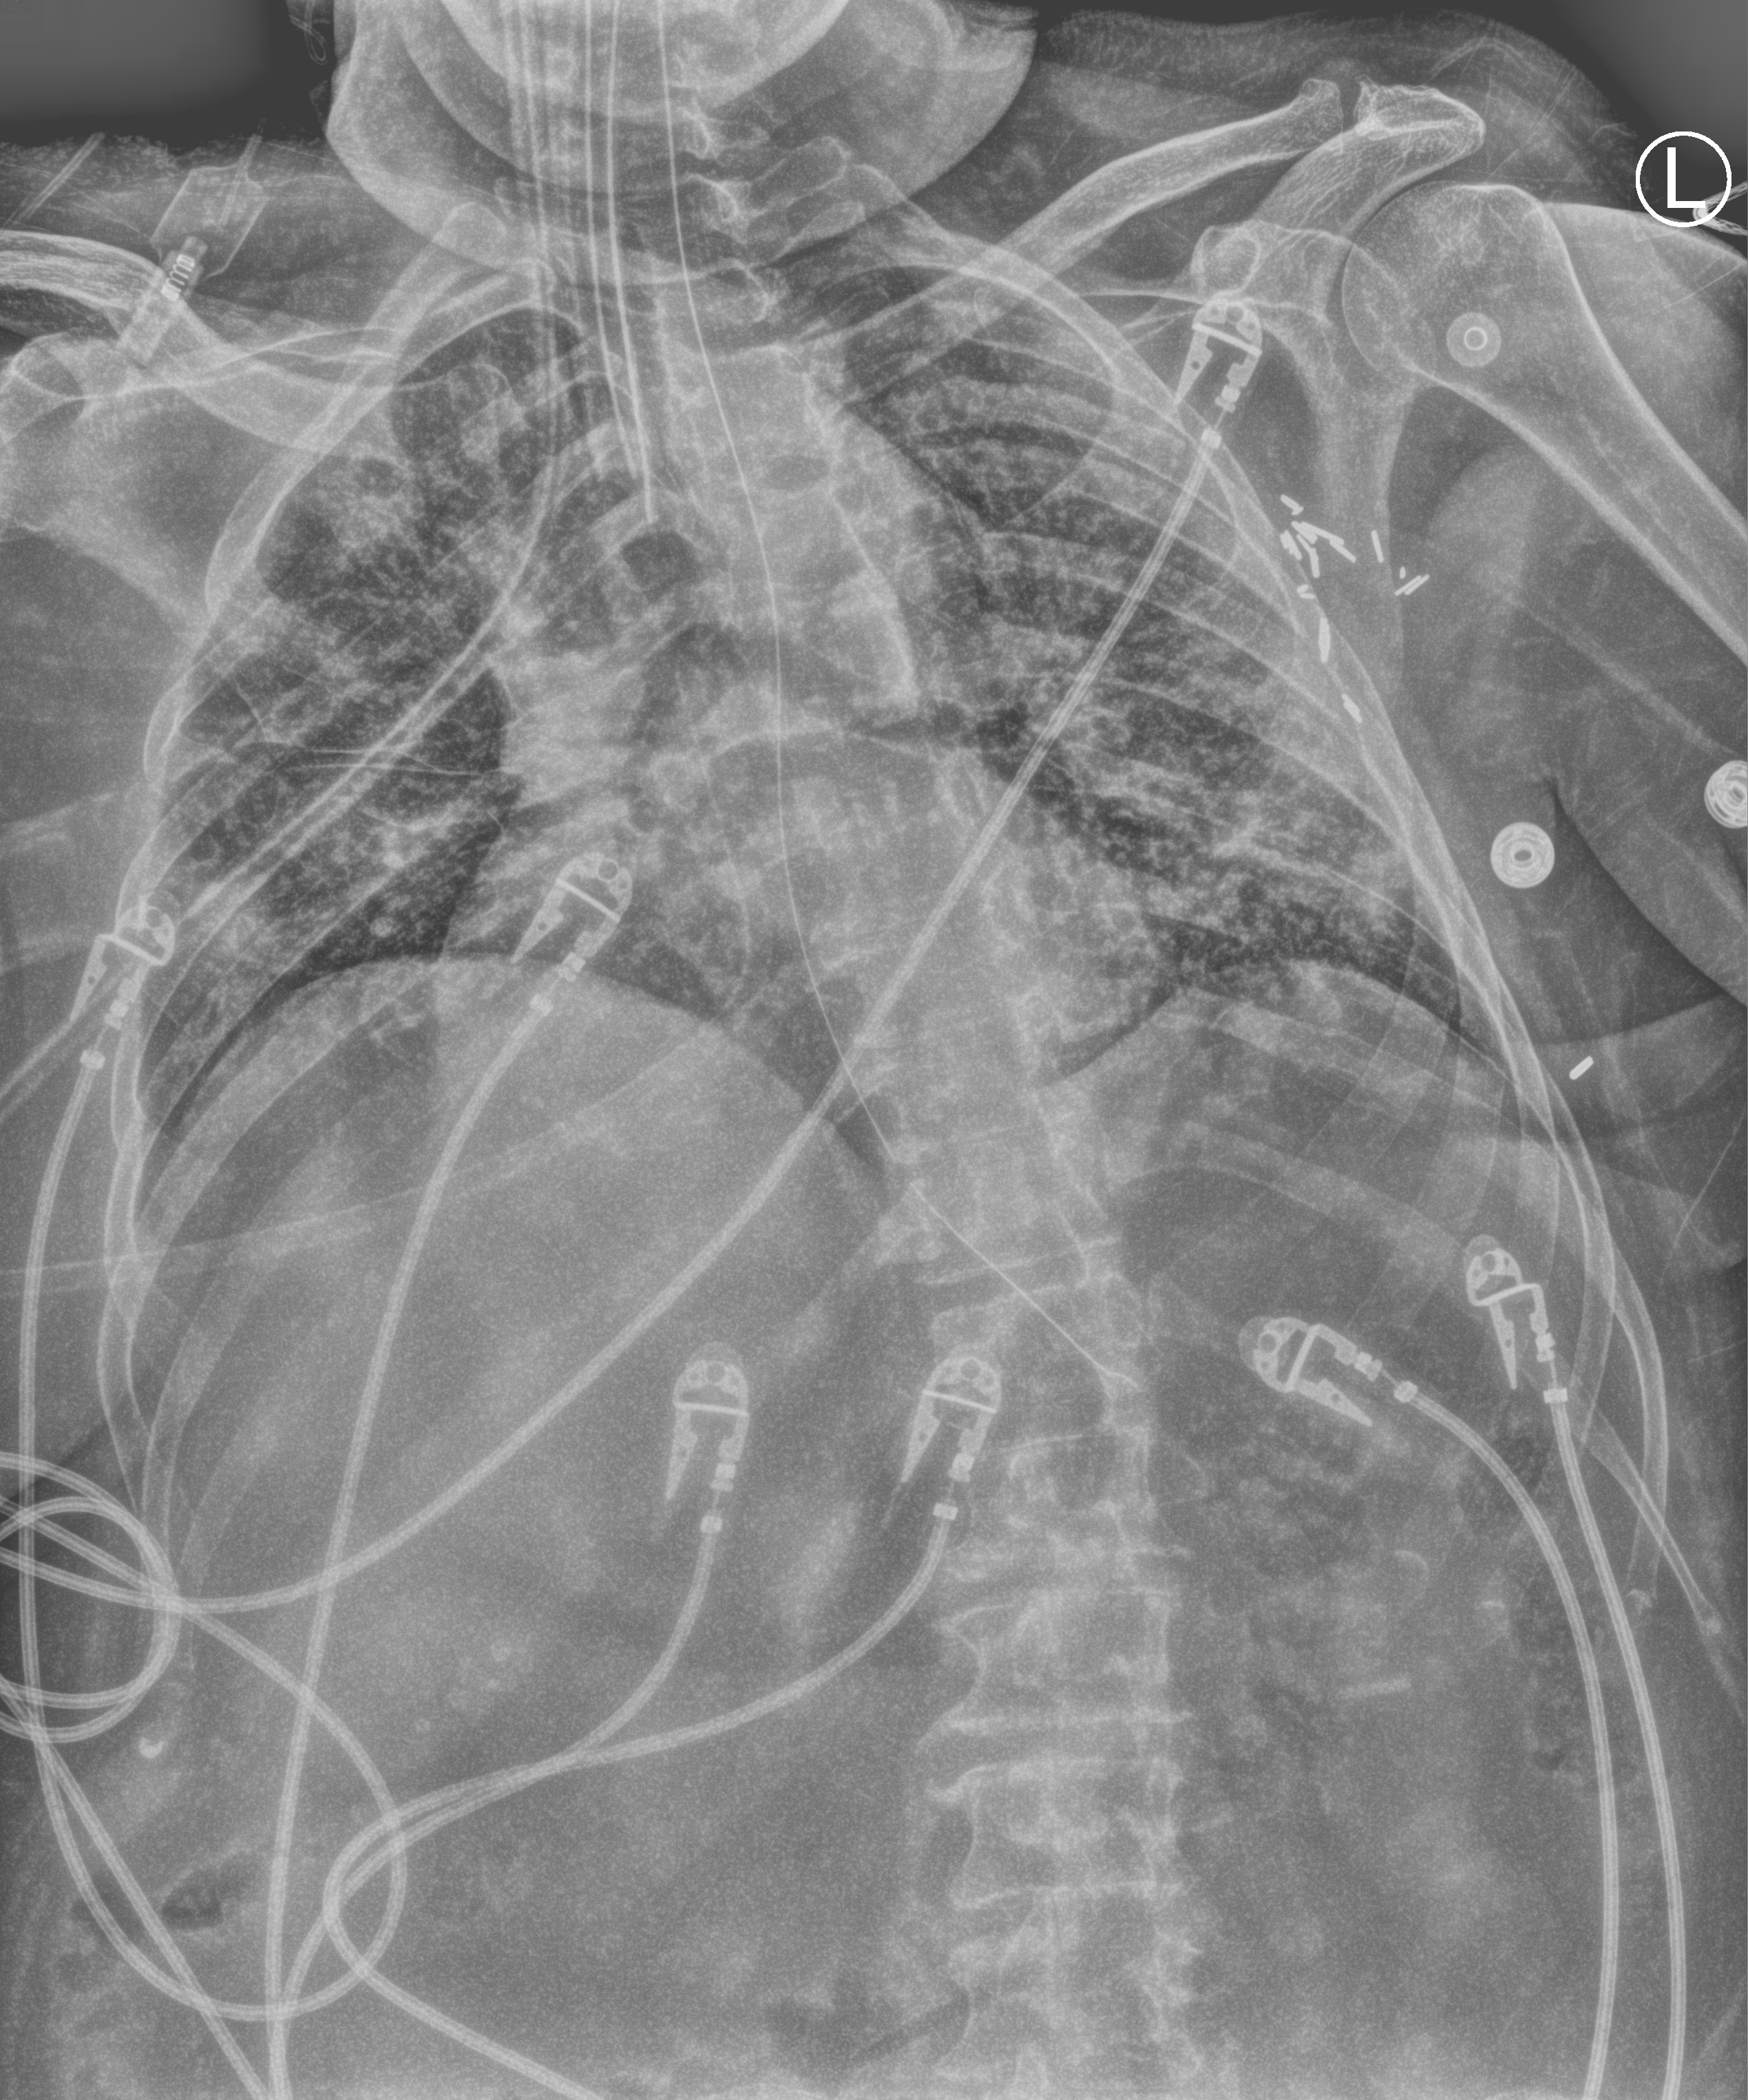
Bedside chest radiograph (computed radiography), anteroposterior (AP) projection. Female patient hospitalised with COVID-19, age 60–74 years.
Hospital-stay facts (about this admission, not read from this image; timing relative to this image not recorded):
- COPD (admission record): no